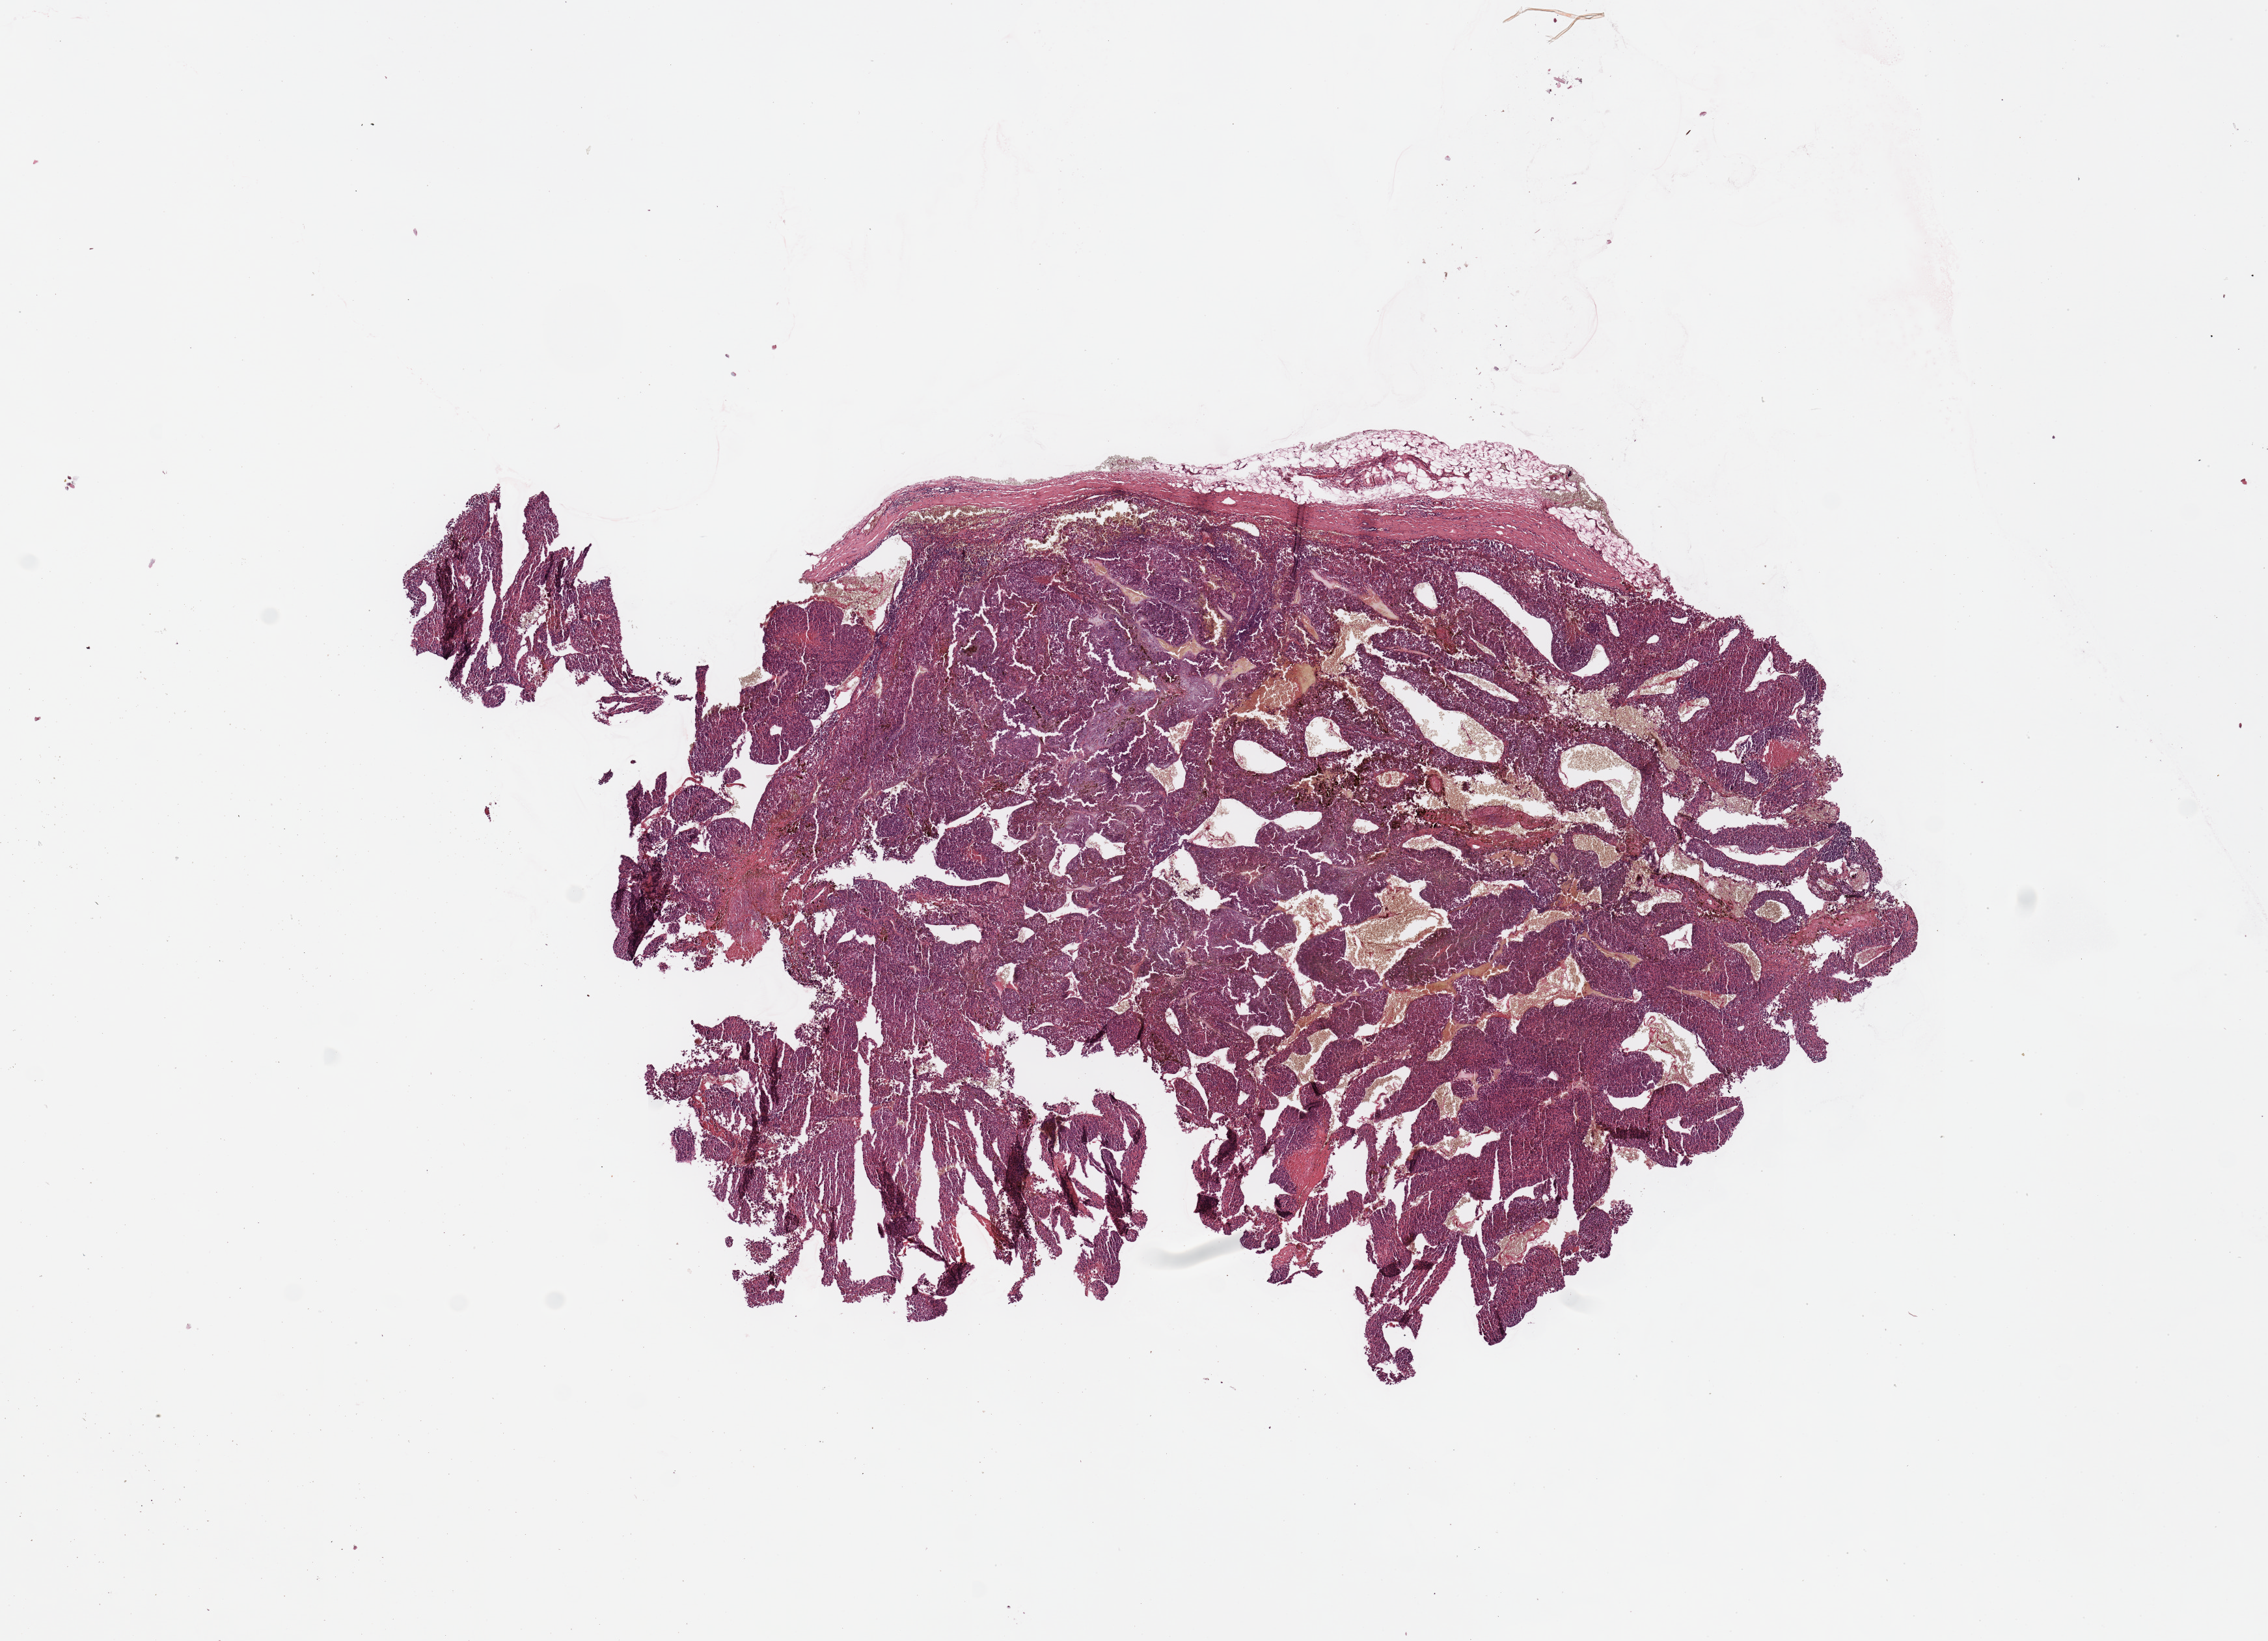
Whole-slide histology image, H&E, whole scanned area (about 13.8 x 10.0 mm, slide scanned at 20x) shown as a low-resolution overview. Melanoma tumour tissue; sampled site not recorded. 60-year-old male patient.
Patient diagnosis (cohort enrolment): cutaneous melanoma (skin). Primary tumour site (as recorded): extremities.